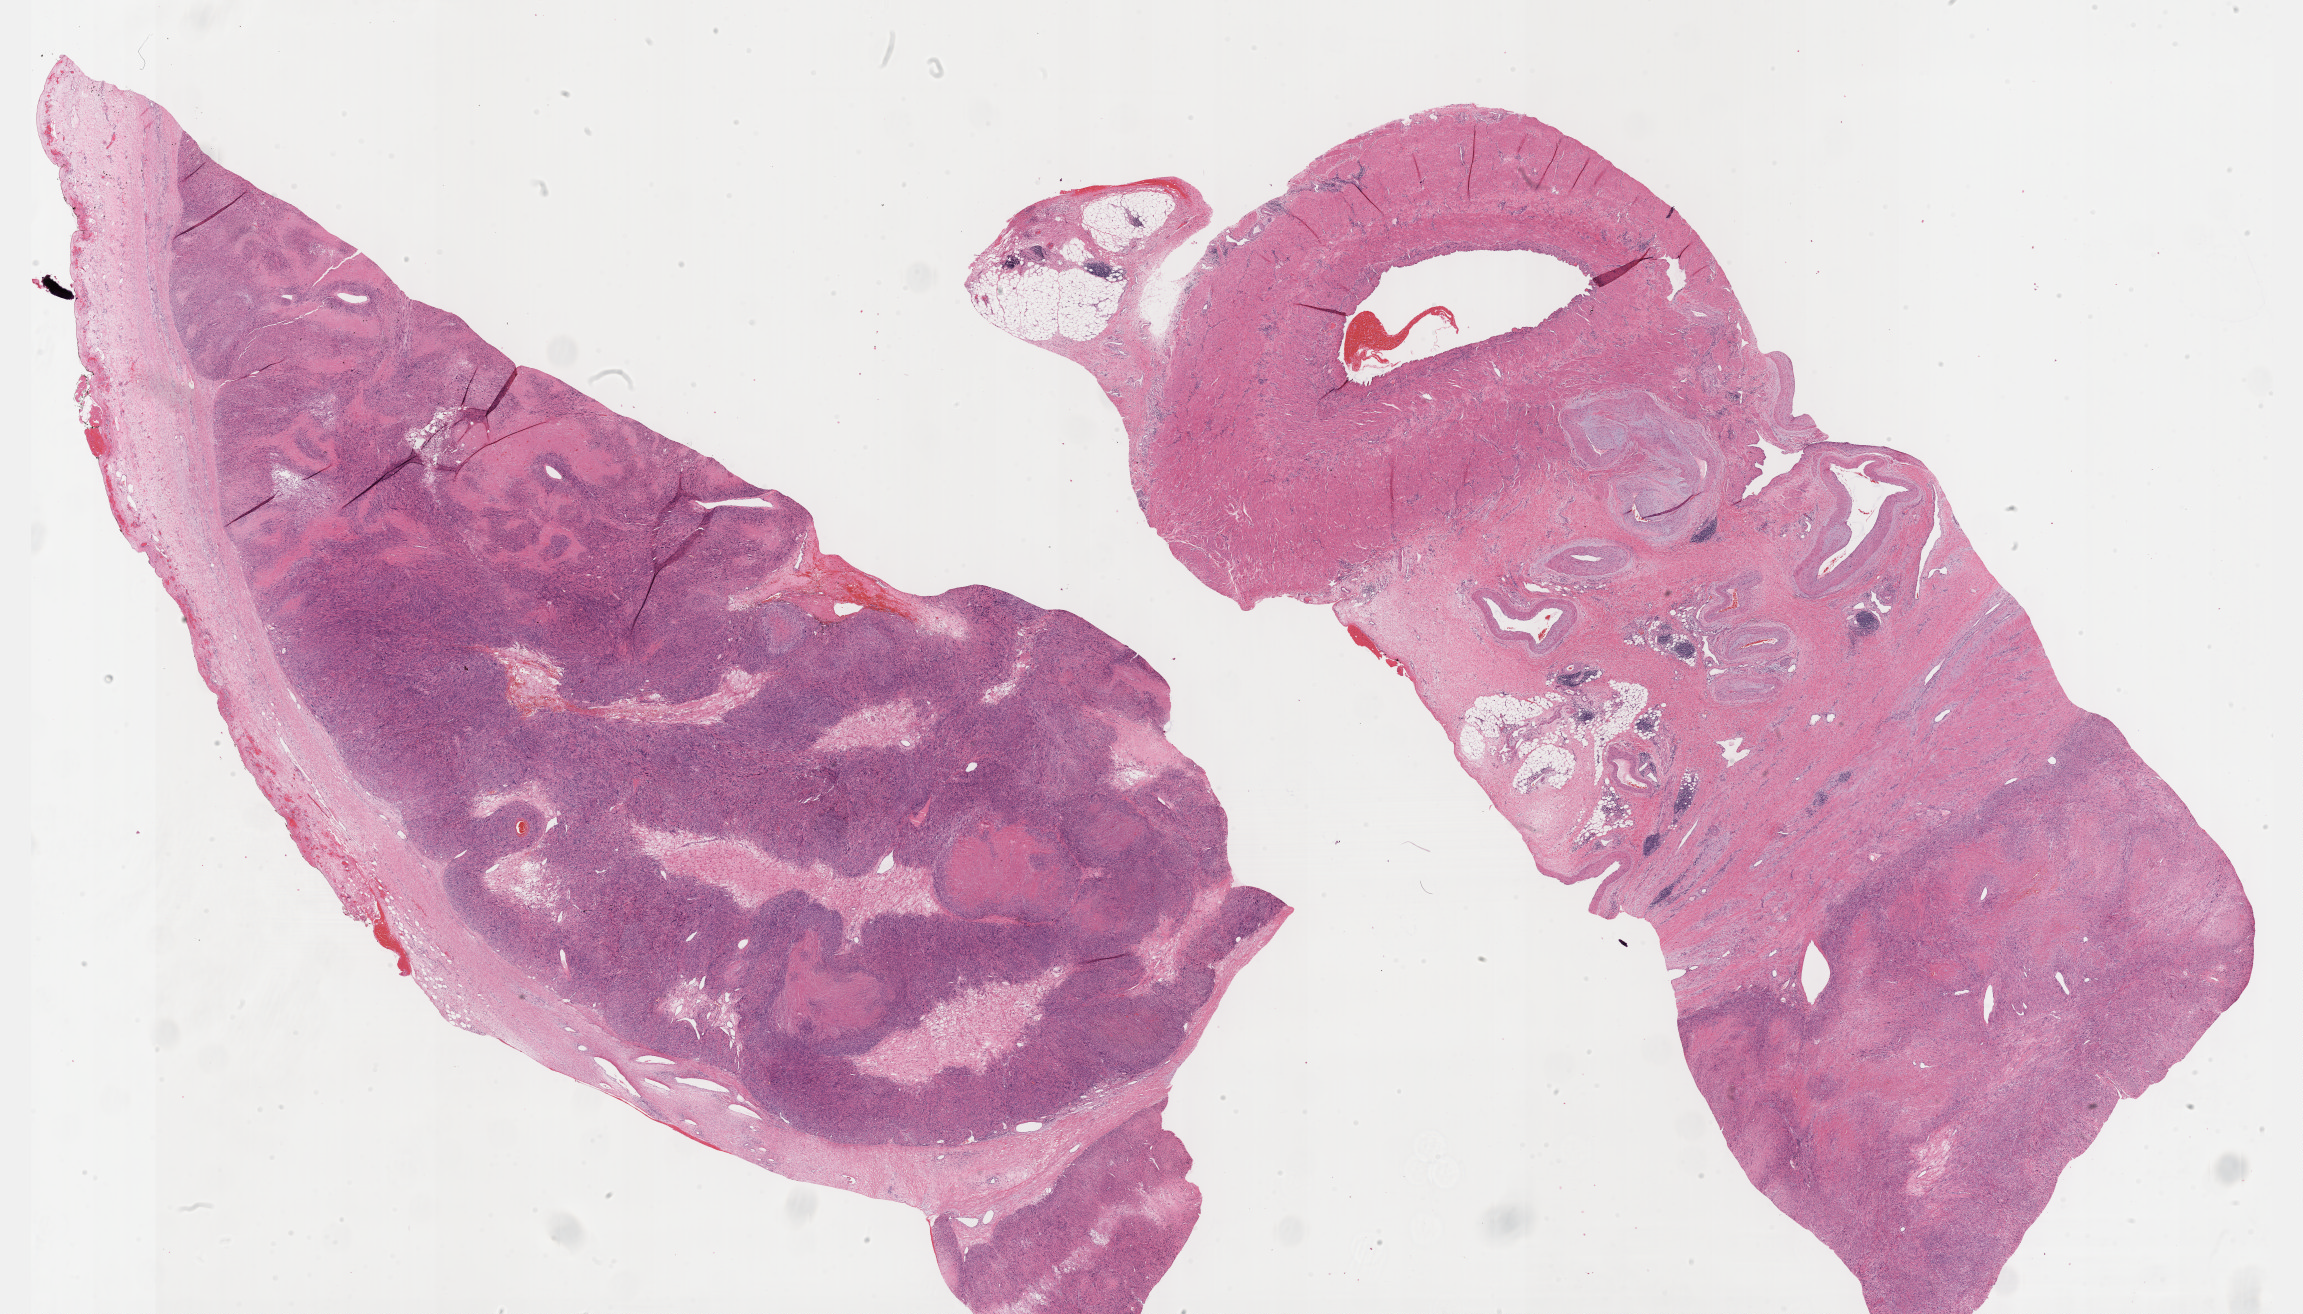
H&E whole-slide image — shown as a low-resolution overview of the whole scanned area (about 37.2 x 21.2 mm, from a 40x scan), FFPE section, sample: primary tumour, retroperitoneum and peritoneum. Female patient; age at initial diagnosis 63 years.
Histologic diagnosis: Leiomyosarcoma, NOS (retroperitoneum).